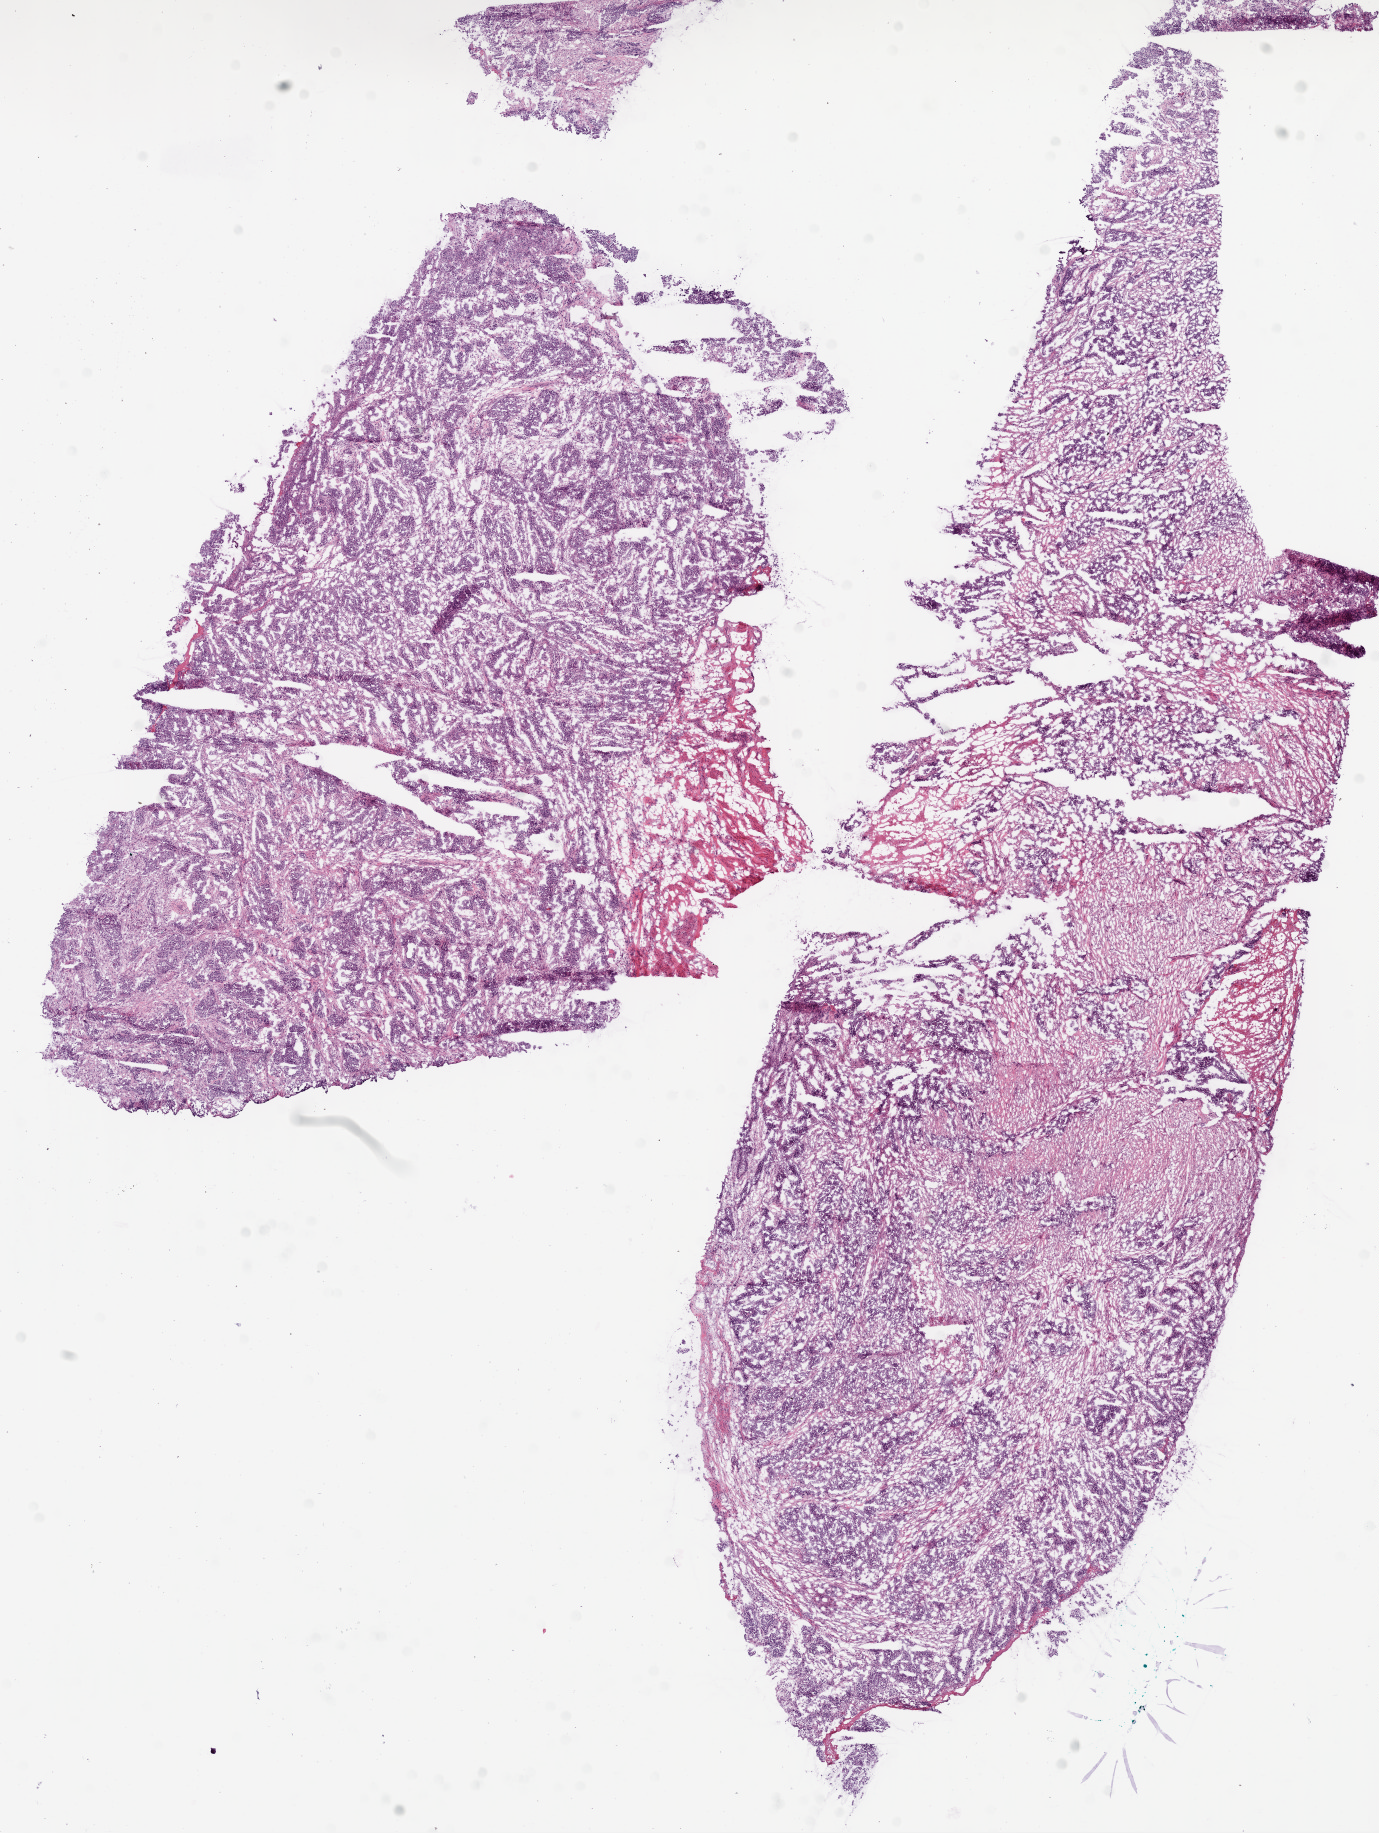
Digitized H&E tissue section (whole slide), shown as a low-resolution overview of the whole scanned area (about 11.1 x 14.8 mm), frozen section, sample: primary tumour, ovary. Female, age 78 years at initial diagnosis.
Pathologic diagnosis: Serous cystadenocarcinoma, NOS.